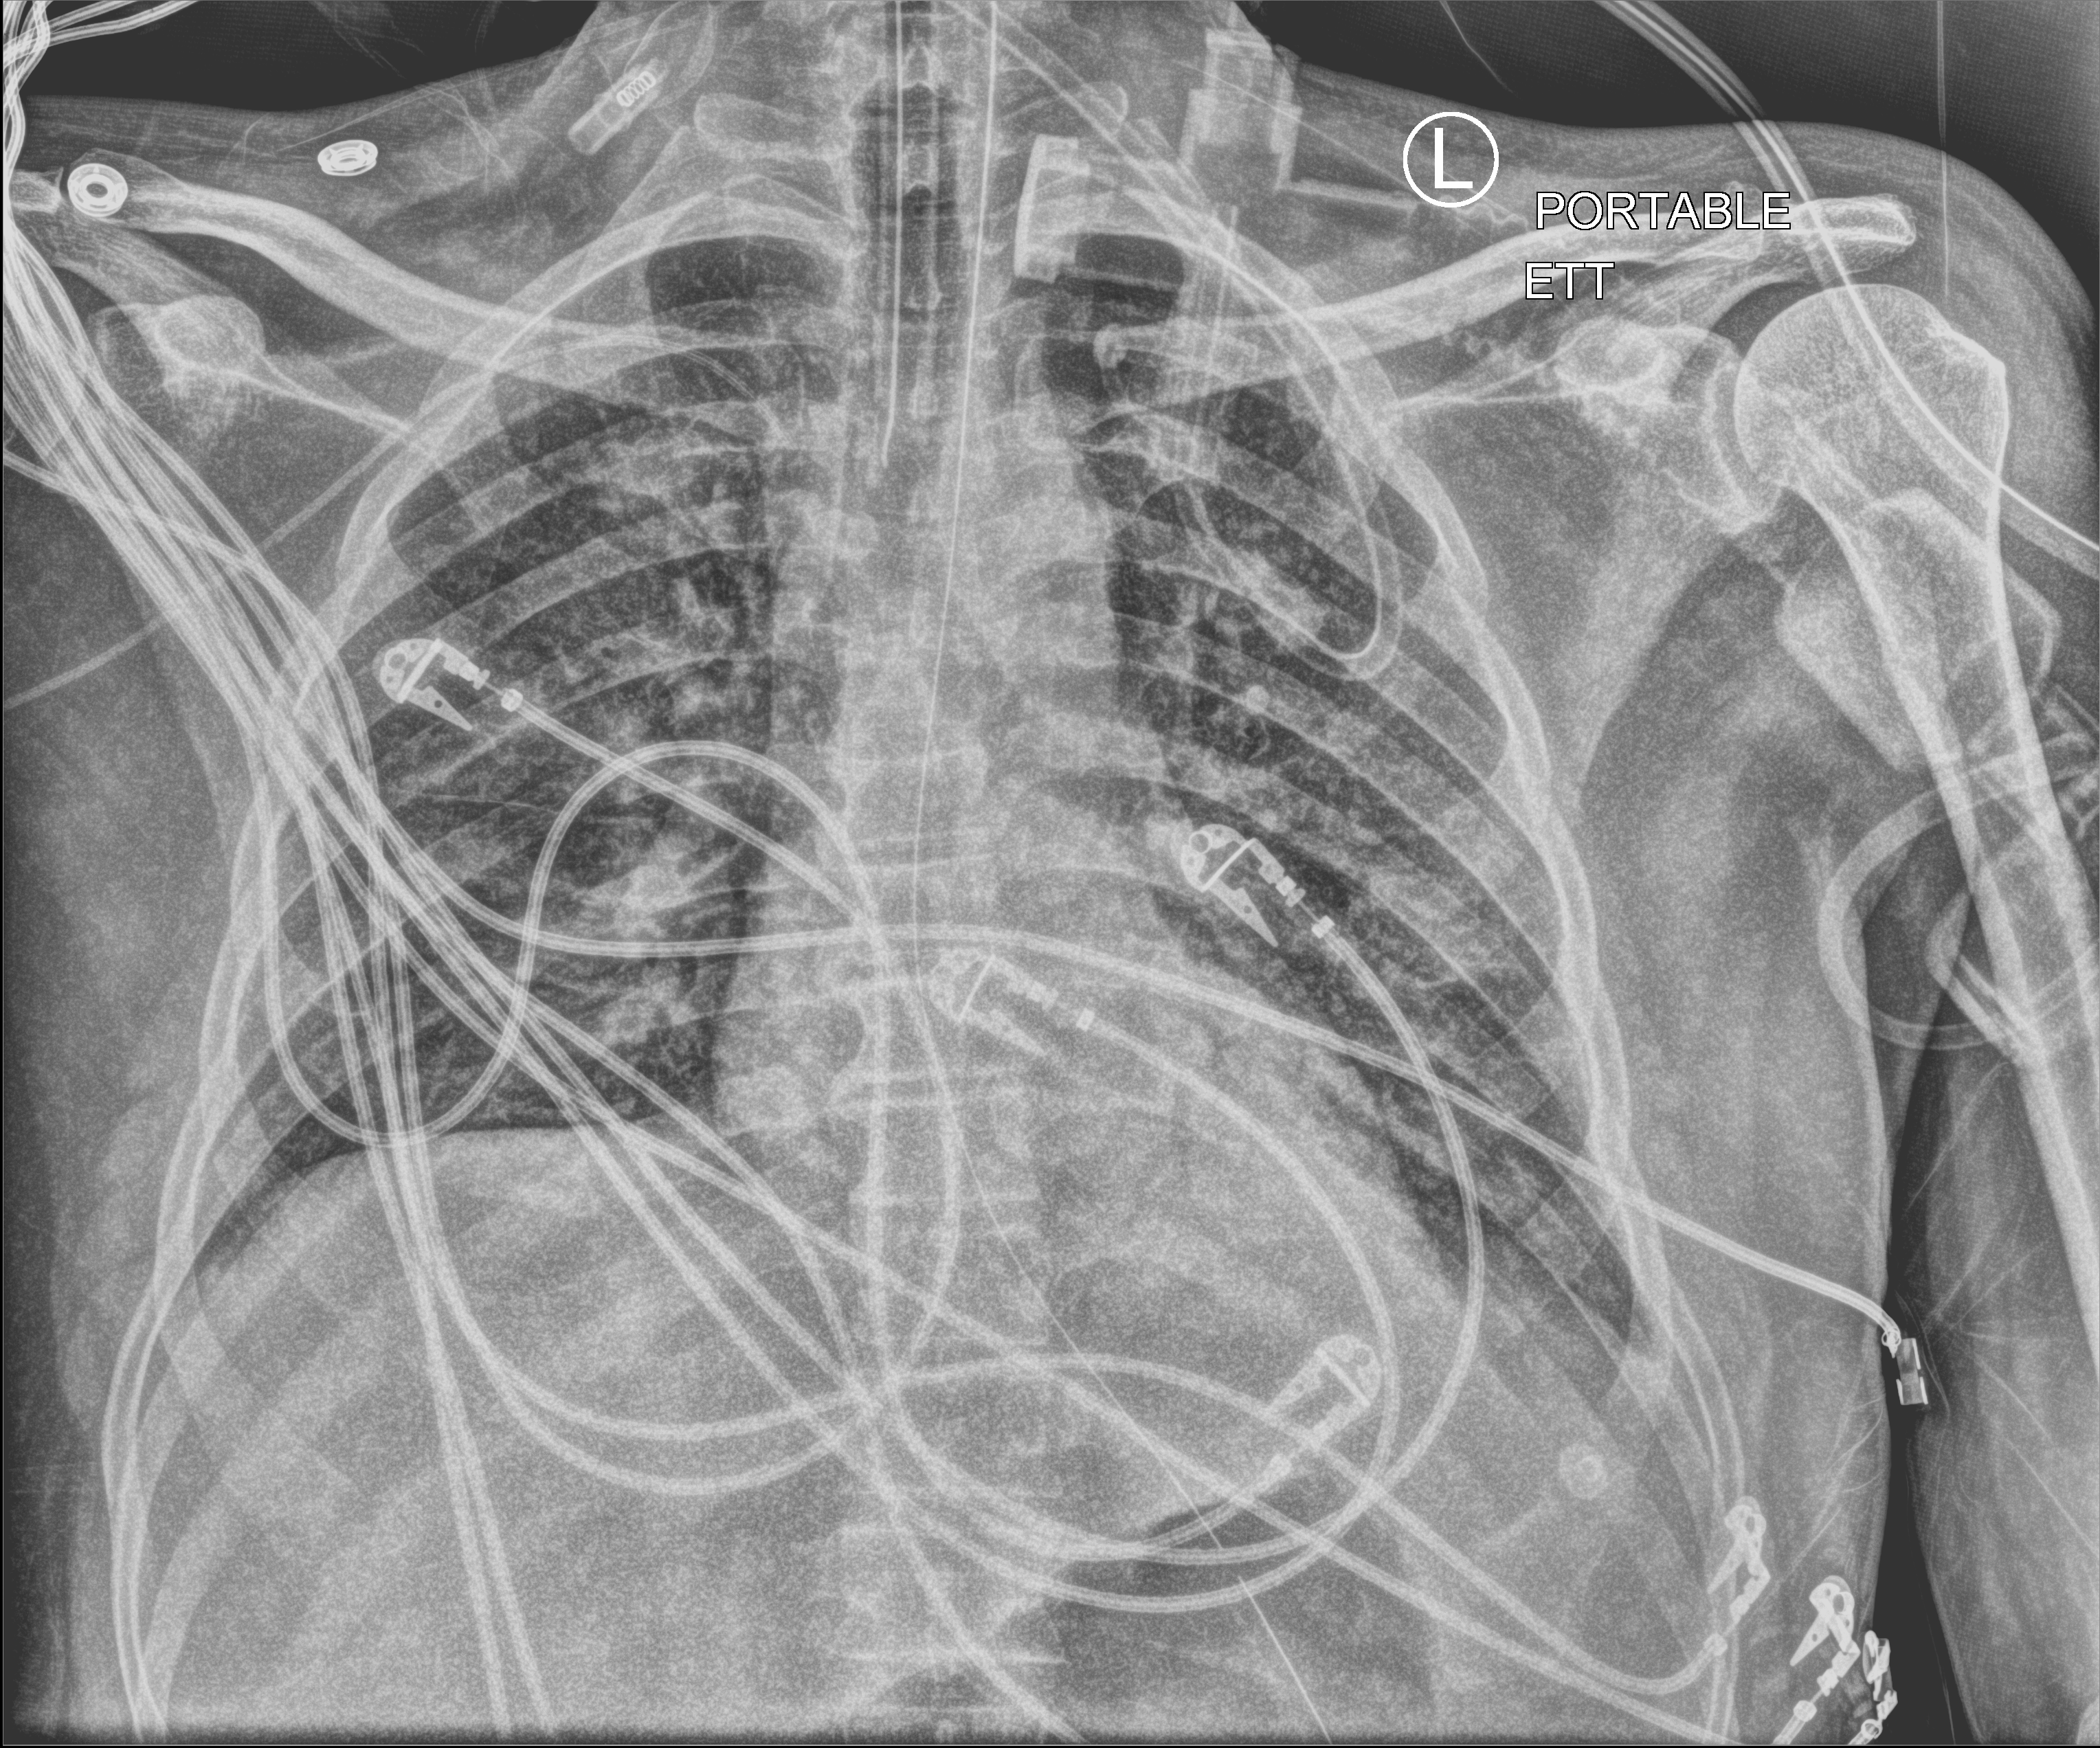
Portable chest radiograph. Male patient hospitalised with COVID-19, age 18–59 years.
From the hospital-stay record, not from the radiograph (when in the stay this image was taken is not recorded): admitted to intensive care during this hospital stay: yes; length of hospital stay: 83 days; mechanically ventilated during this hospital stay: yes.